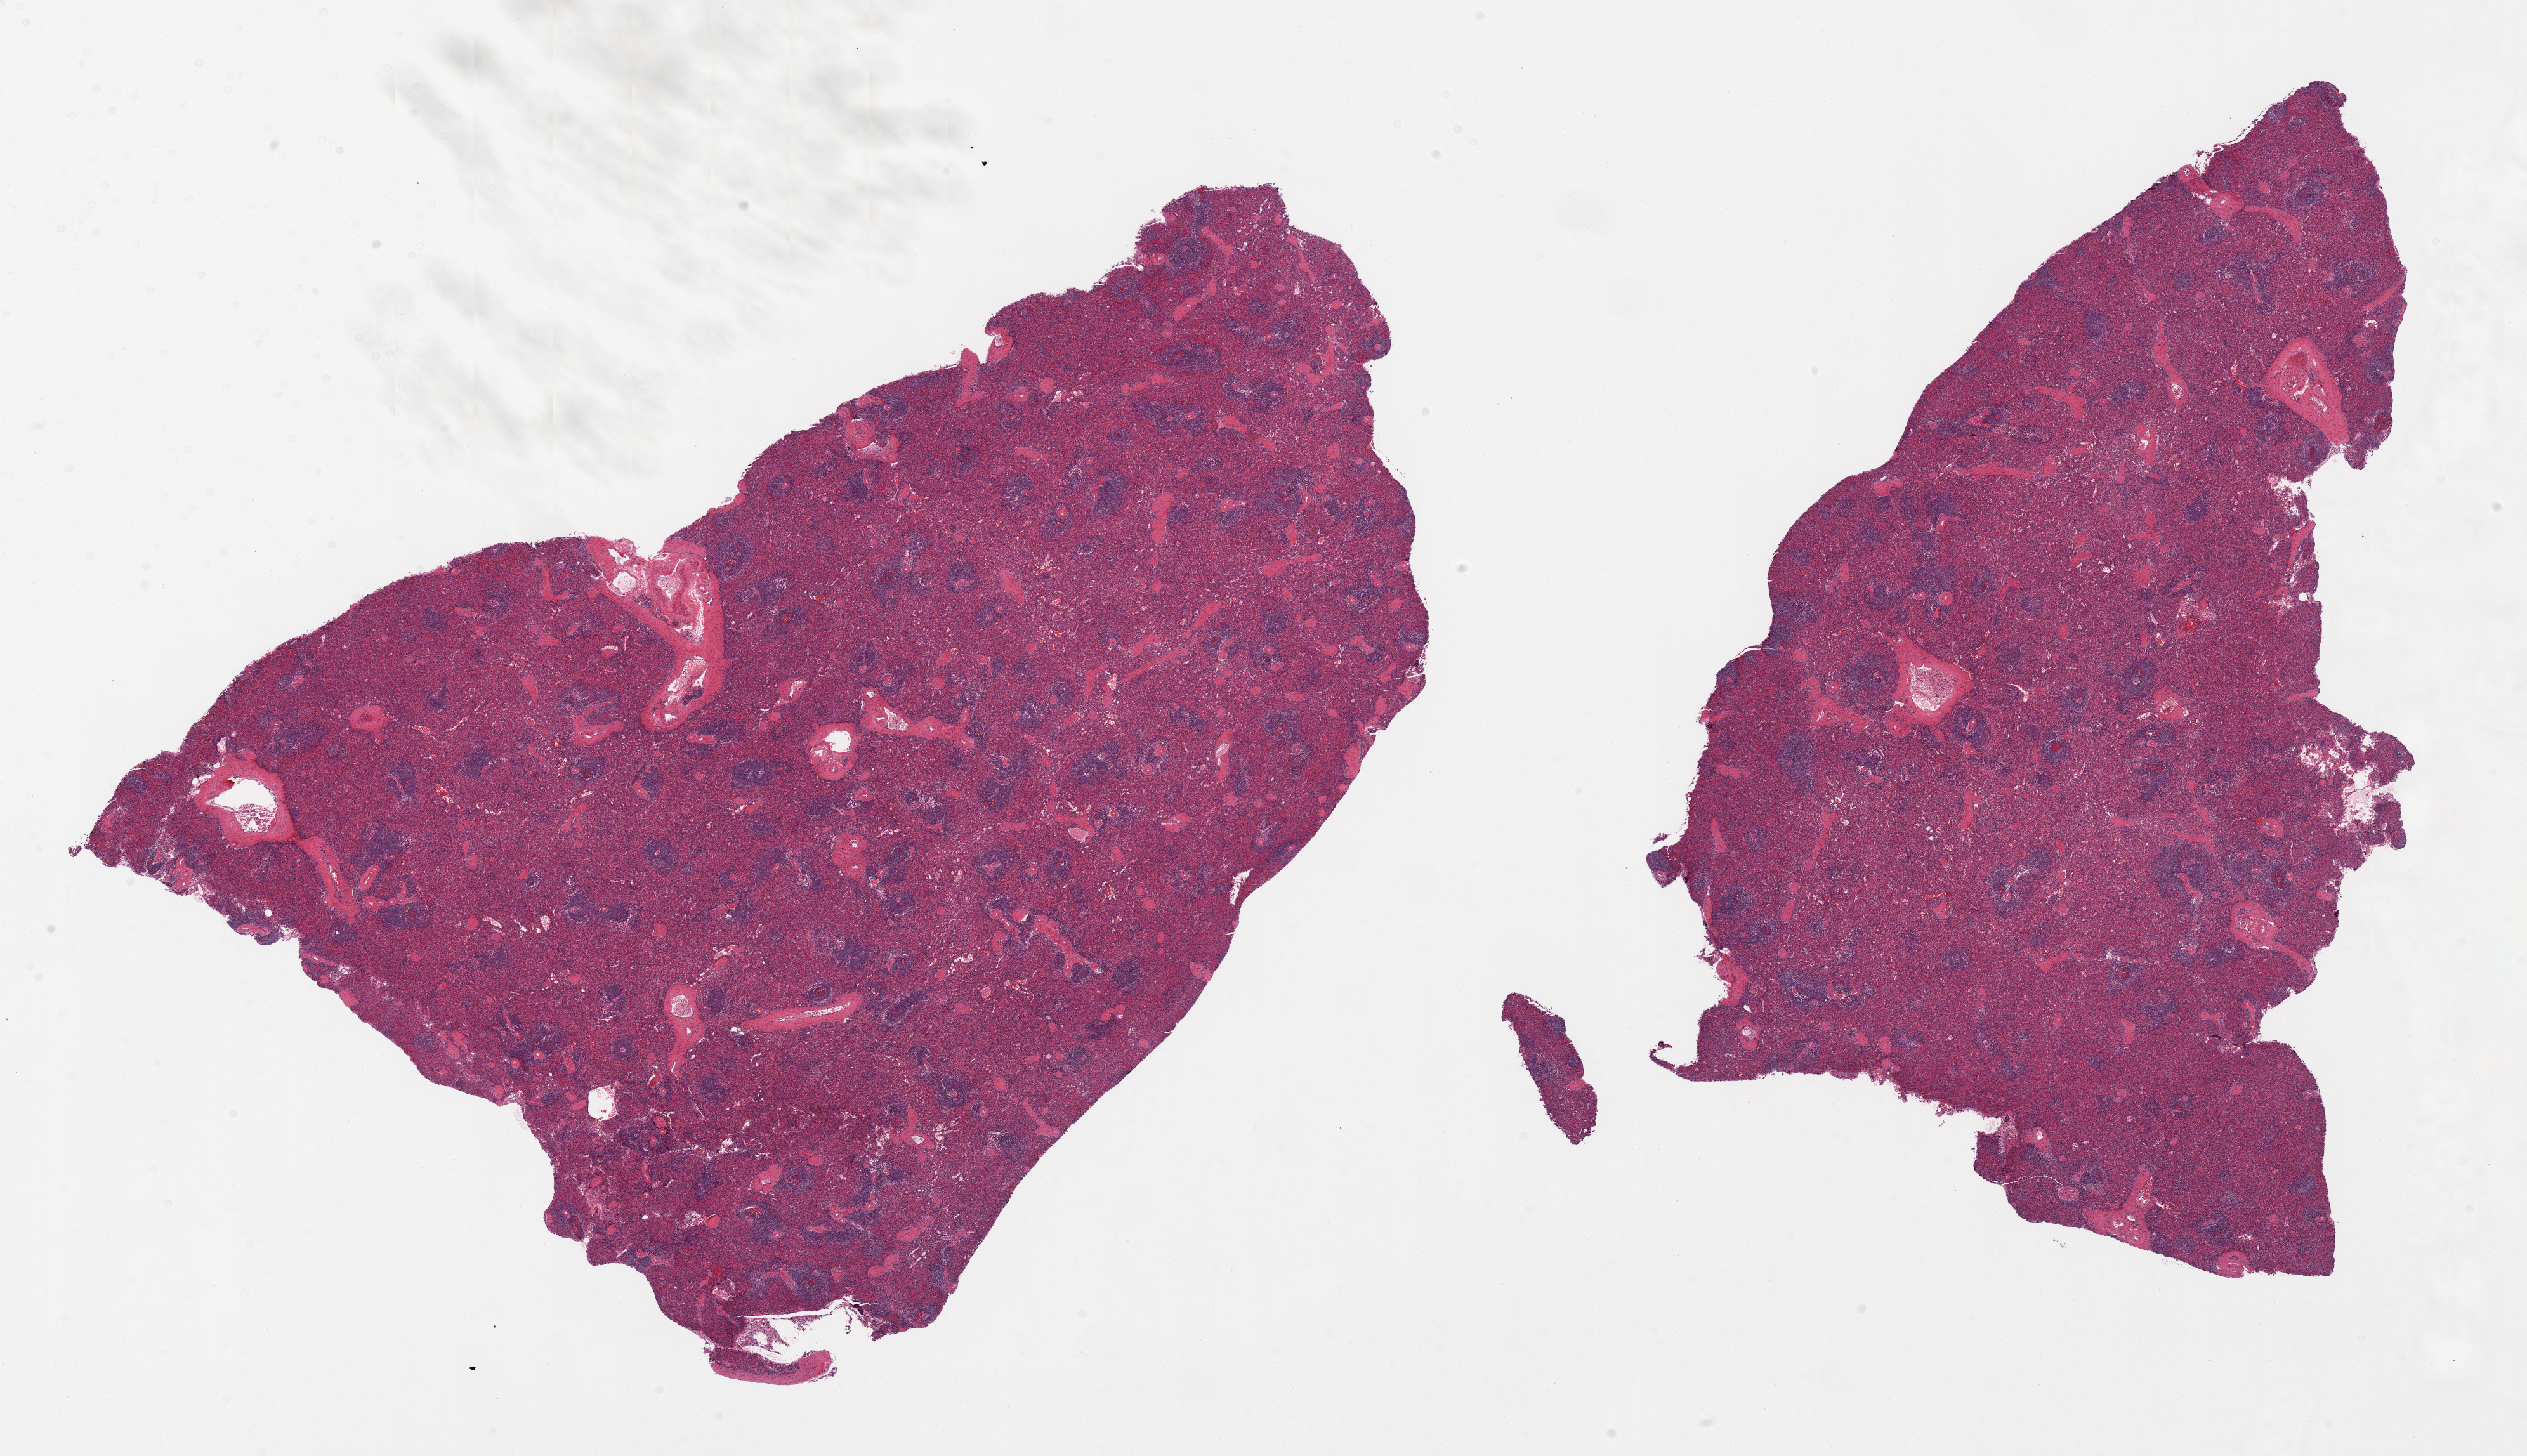
Whole-slide image, haematoxylin and eosin stain, shown as a low-resolution overview of the whole scanned area (about 31.5 x 18.2 mm); PAXgene-fixed, paraffin-embedded tissue; sampled site (target tissue): spleen; donor tissue sample. Donor sex: male.
Reviewer comment on this tissue sample: 2 pieces.